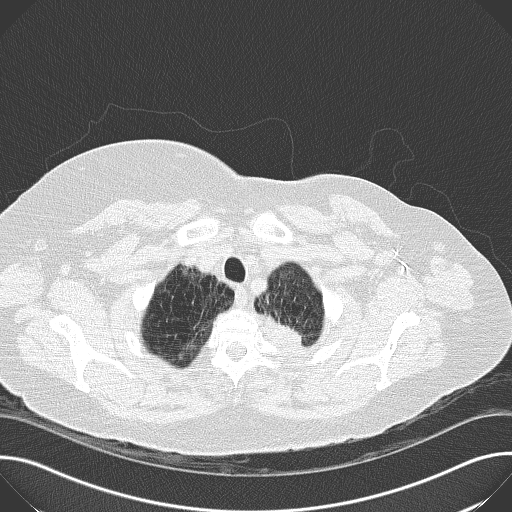
Low-dose screening chest CT, one axial slice; slice 152 of 169 in the series (ordered by position); reconstruction kernel B50f; lung window (W 1500 / L -600 HU); 512 × 512 image matrix, field of view 380 × 380 mm.
Outlined on this slice (expert manual segmentation):
- lesion 1 (tumor, upper lobe of left lung): bounding box <278,323,302,343> (left, top, right, bottom; pixels)